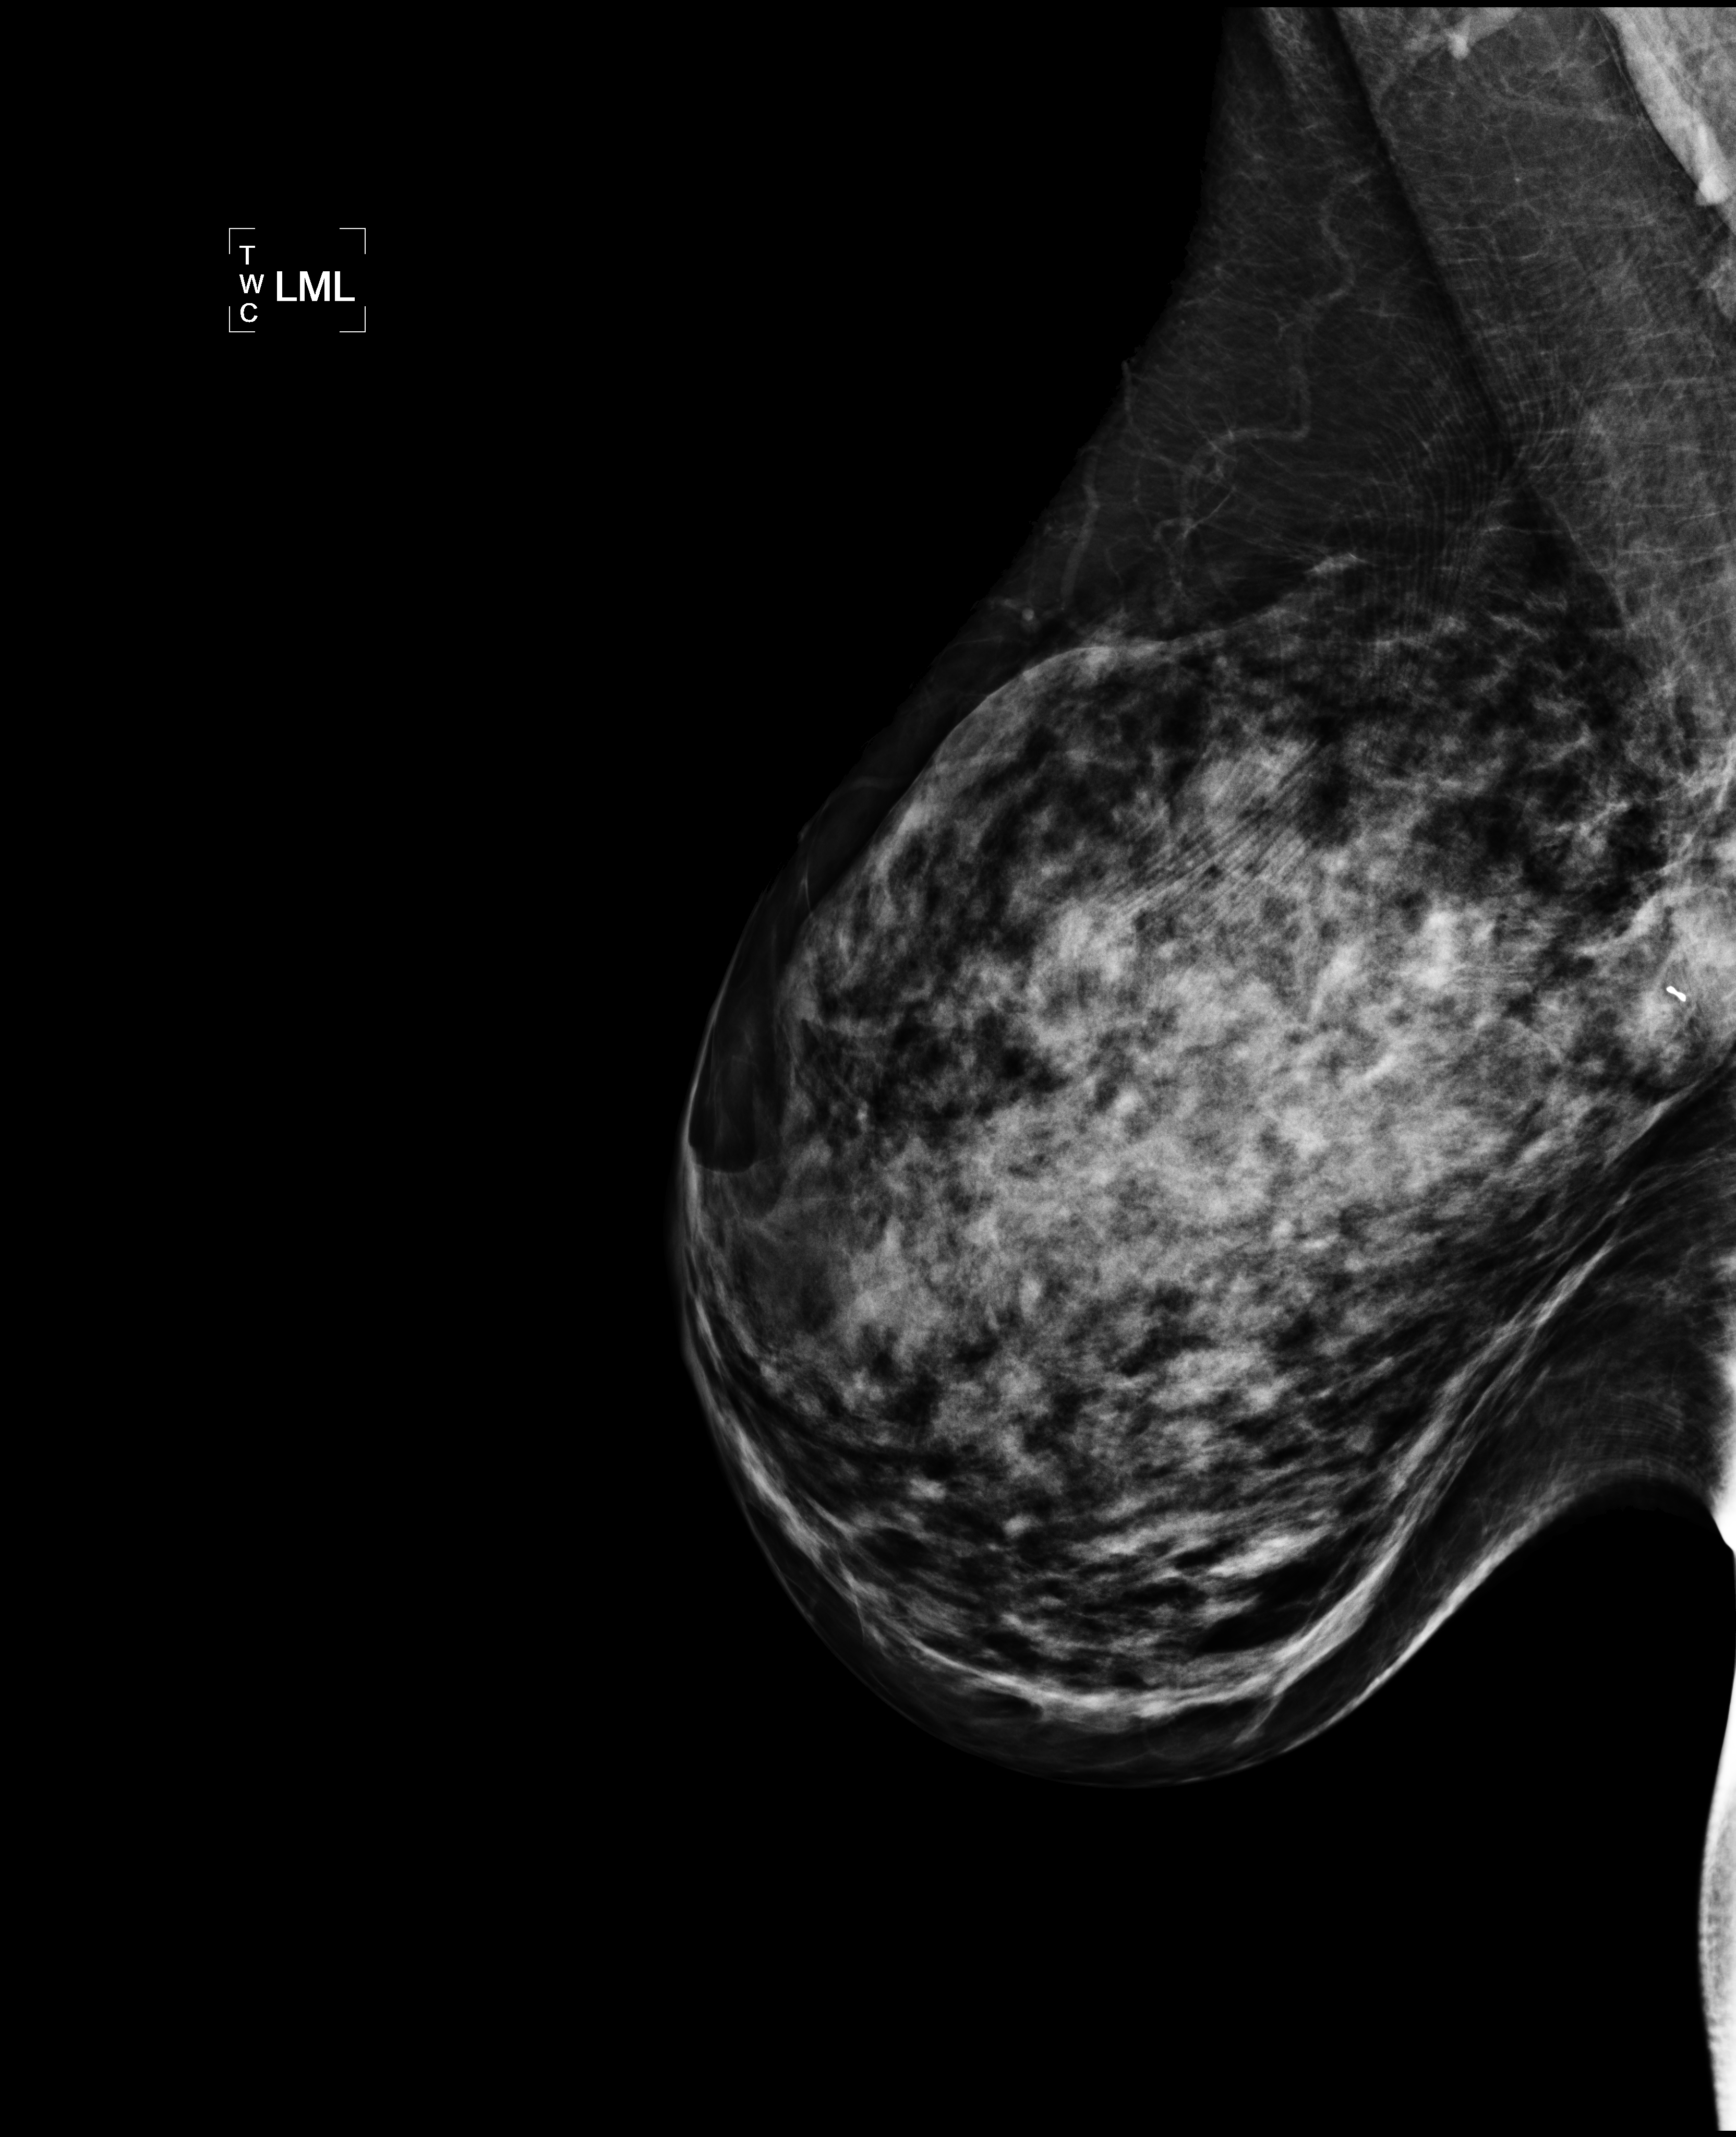
Diagnostic work-up study; compressed breast thickness 74 mm. Patient: female, 43 years.
Image type: full-field digital mammogram. Breast: left. Projection: ML view.